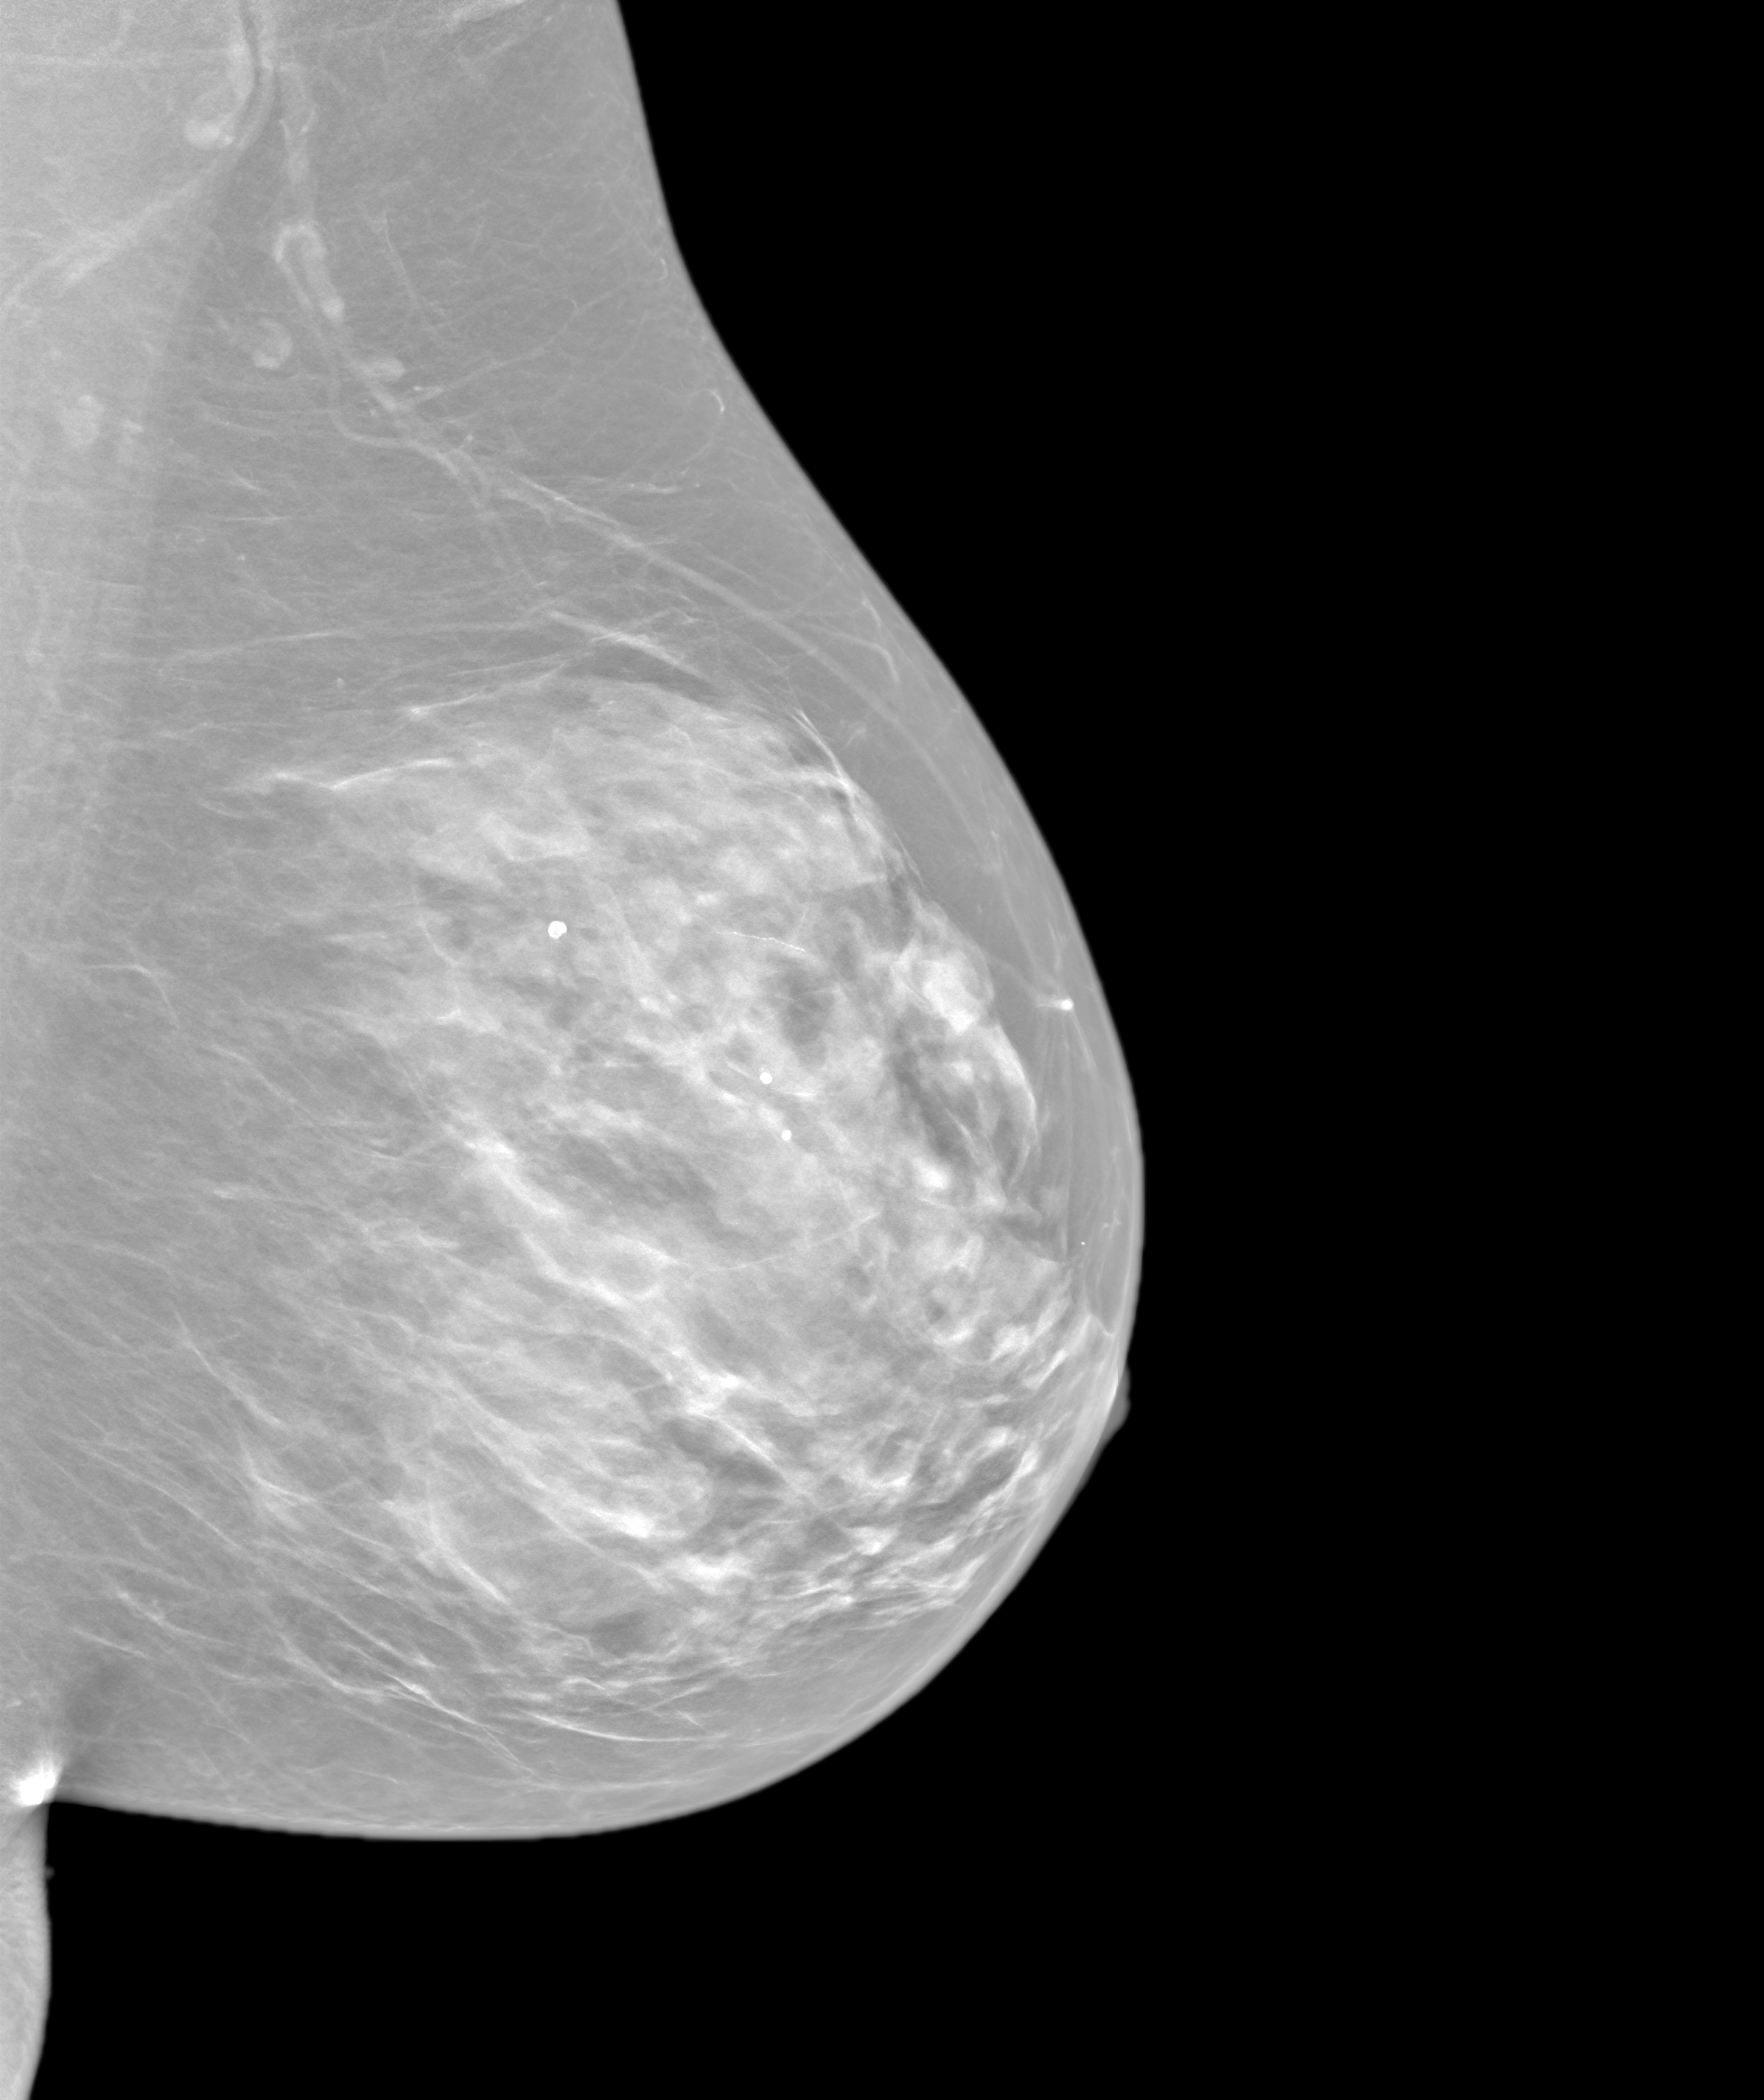
Annual screening mammography examination. Female patient, age 66 years.
Image type: synthesized 2-D view from tomosynthesis. Breast: left. Projection: medio-lateral oblique projection.